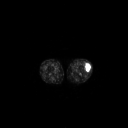
FDG PET of an extremity soft-tissue mass (from a PET/CT study), one axial slice; position 174 of 223 along the scan axis; 128 × 128 image matrix. Female patient, age 16 years. From the clinical record (not read from this slice): histological type: spindle cell suggestive of biphasic synovial sarcoma; grade: intermediate; site of the primary tumour: left knee.
Annotated regions visible in this slice (expert contour drawn on MRI and transferred to this co-registered scan by the dataset authors):
- gross tumour volume including surrounding oedema: box from (x=84, y=62) to (x=91, y=72) px
- gross tumour volume (mass): (x=85, y=62)–(x=91, y=72)